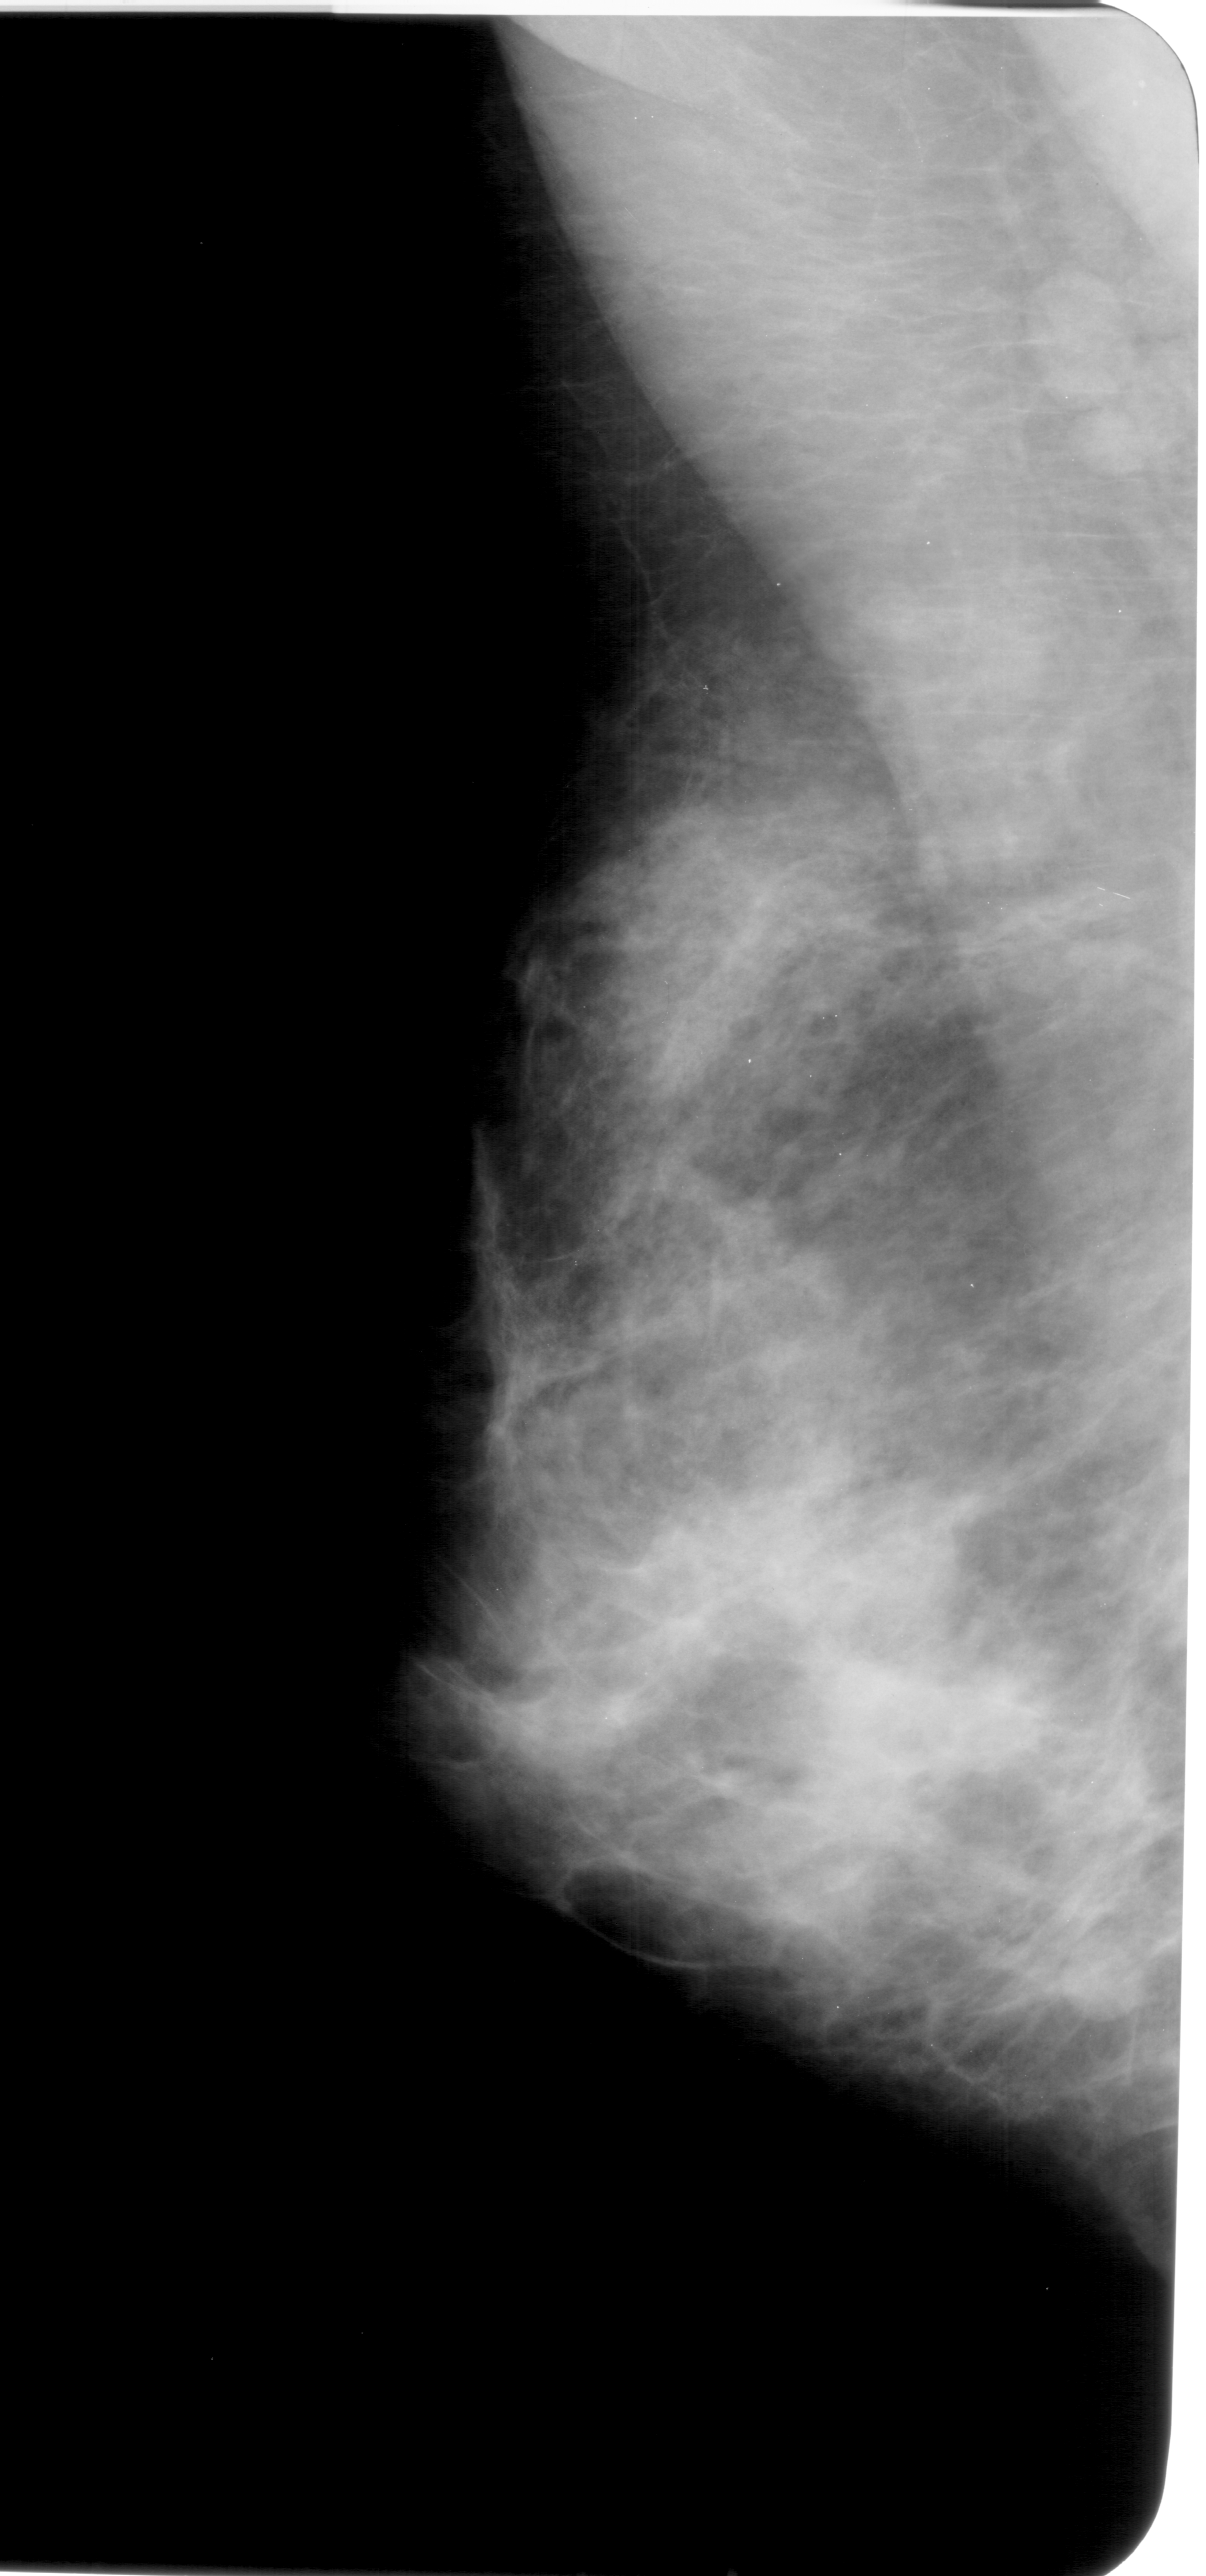
Digitized screen-film mammogram; left breast; mediolateral oblique (MLO) view; breast composition: extremely dense (BI-RADS density category 4 of 4).
Abnormality record for this image: mass, shape round, margins circumscribed; BI-RADS assessment category 4; pathology result (as recorded, not read from the image): benign.